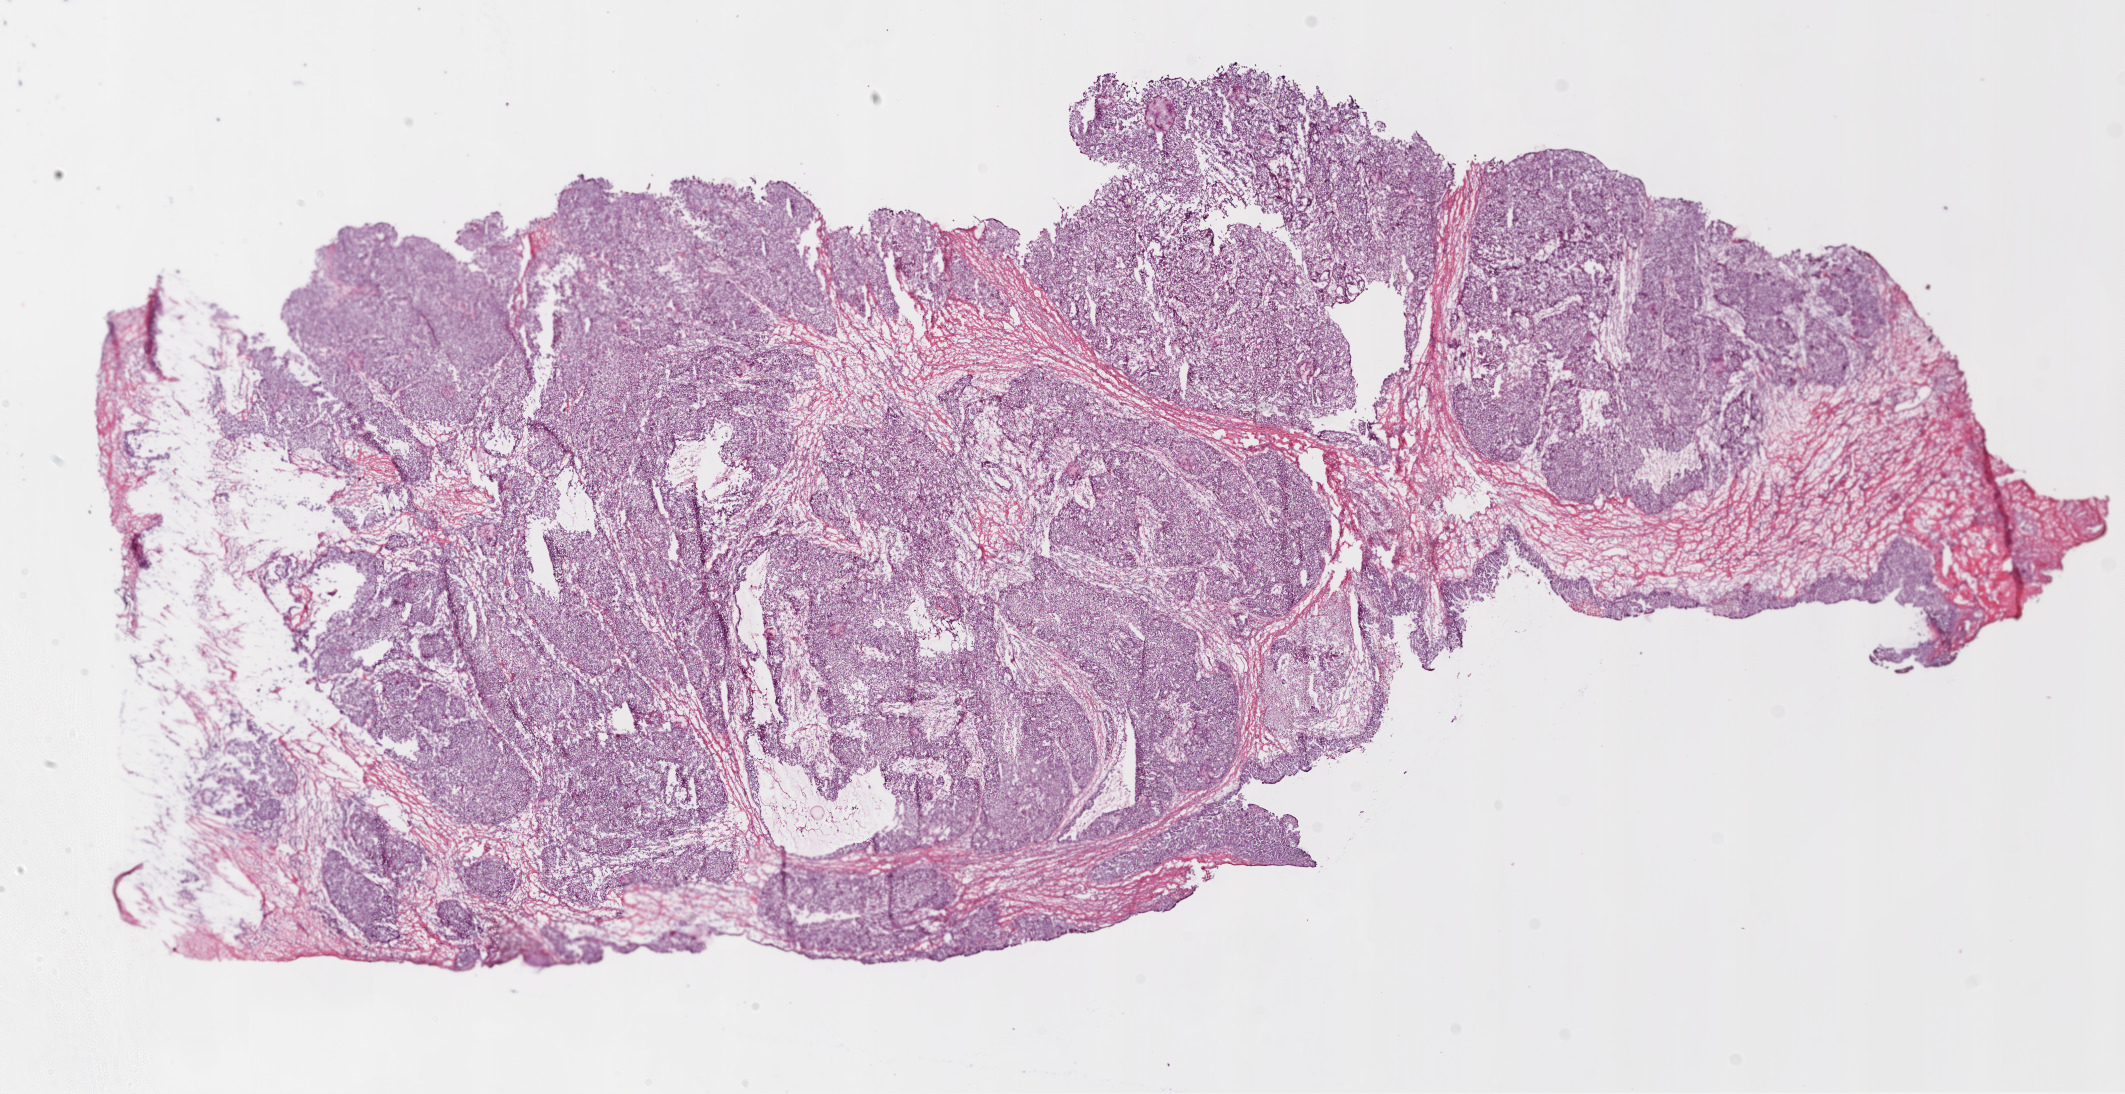
Whole-slide histology image, H&E-stained — shown as a low-resolution overview of the whole scanned area (about 17.1 x 8.8 mm), frozen section from the bottom of the tissue portion, sample: primary tumour, ovary. Female, age 61 years at initial diagnosis. Histologic grade: G3 (poorly differentiated). Slide review estimates, as recorded: tumour cells 90%, tumour nuclei 90%, normal cells 0%, stromal cells 10%, necrosis 0%.
Histologic diagnosis: Serous cystadenocarcinoma, NOS. Laterality: bilateral. FIGO stage: IIIC.